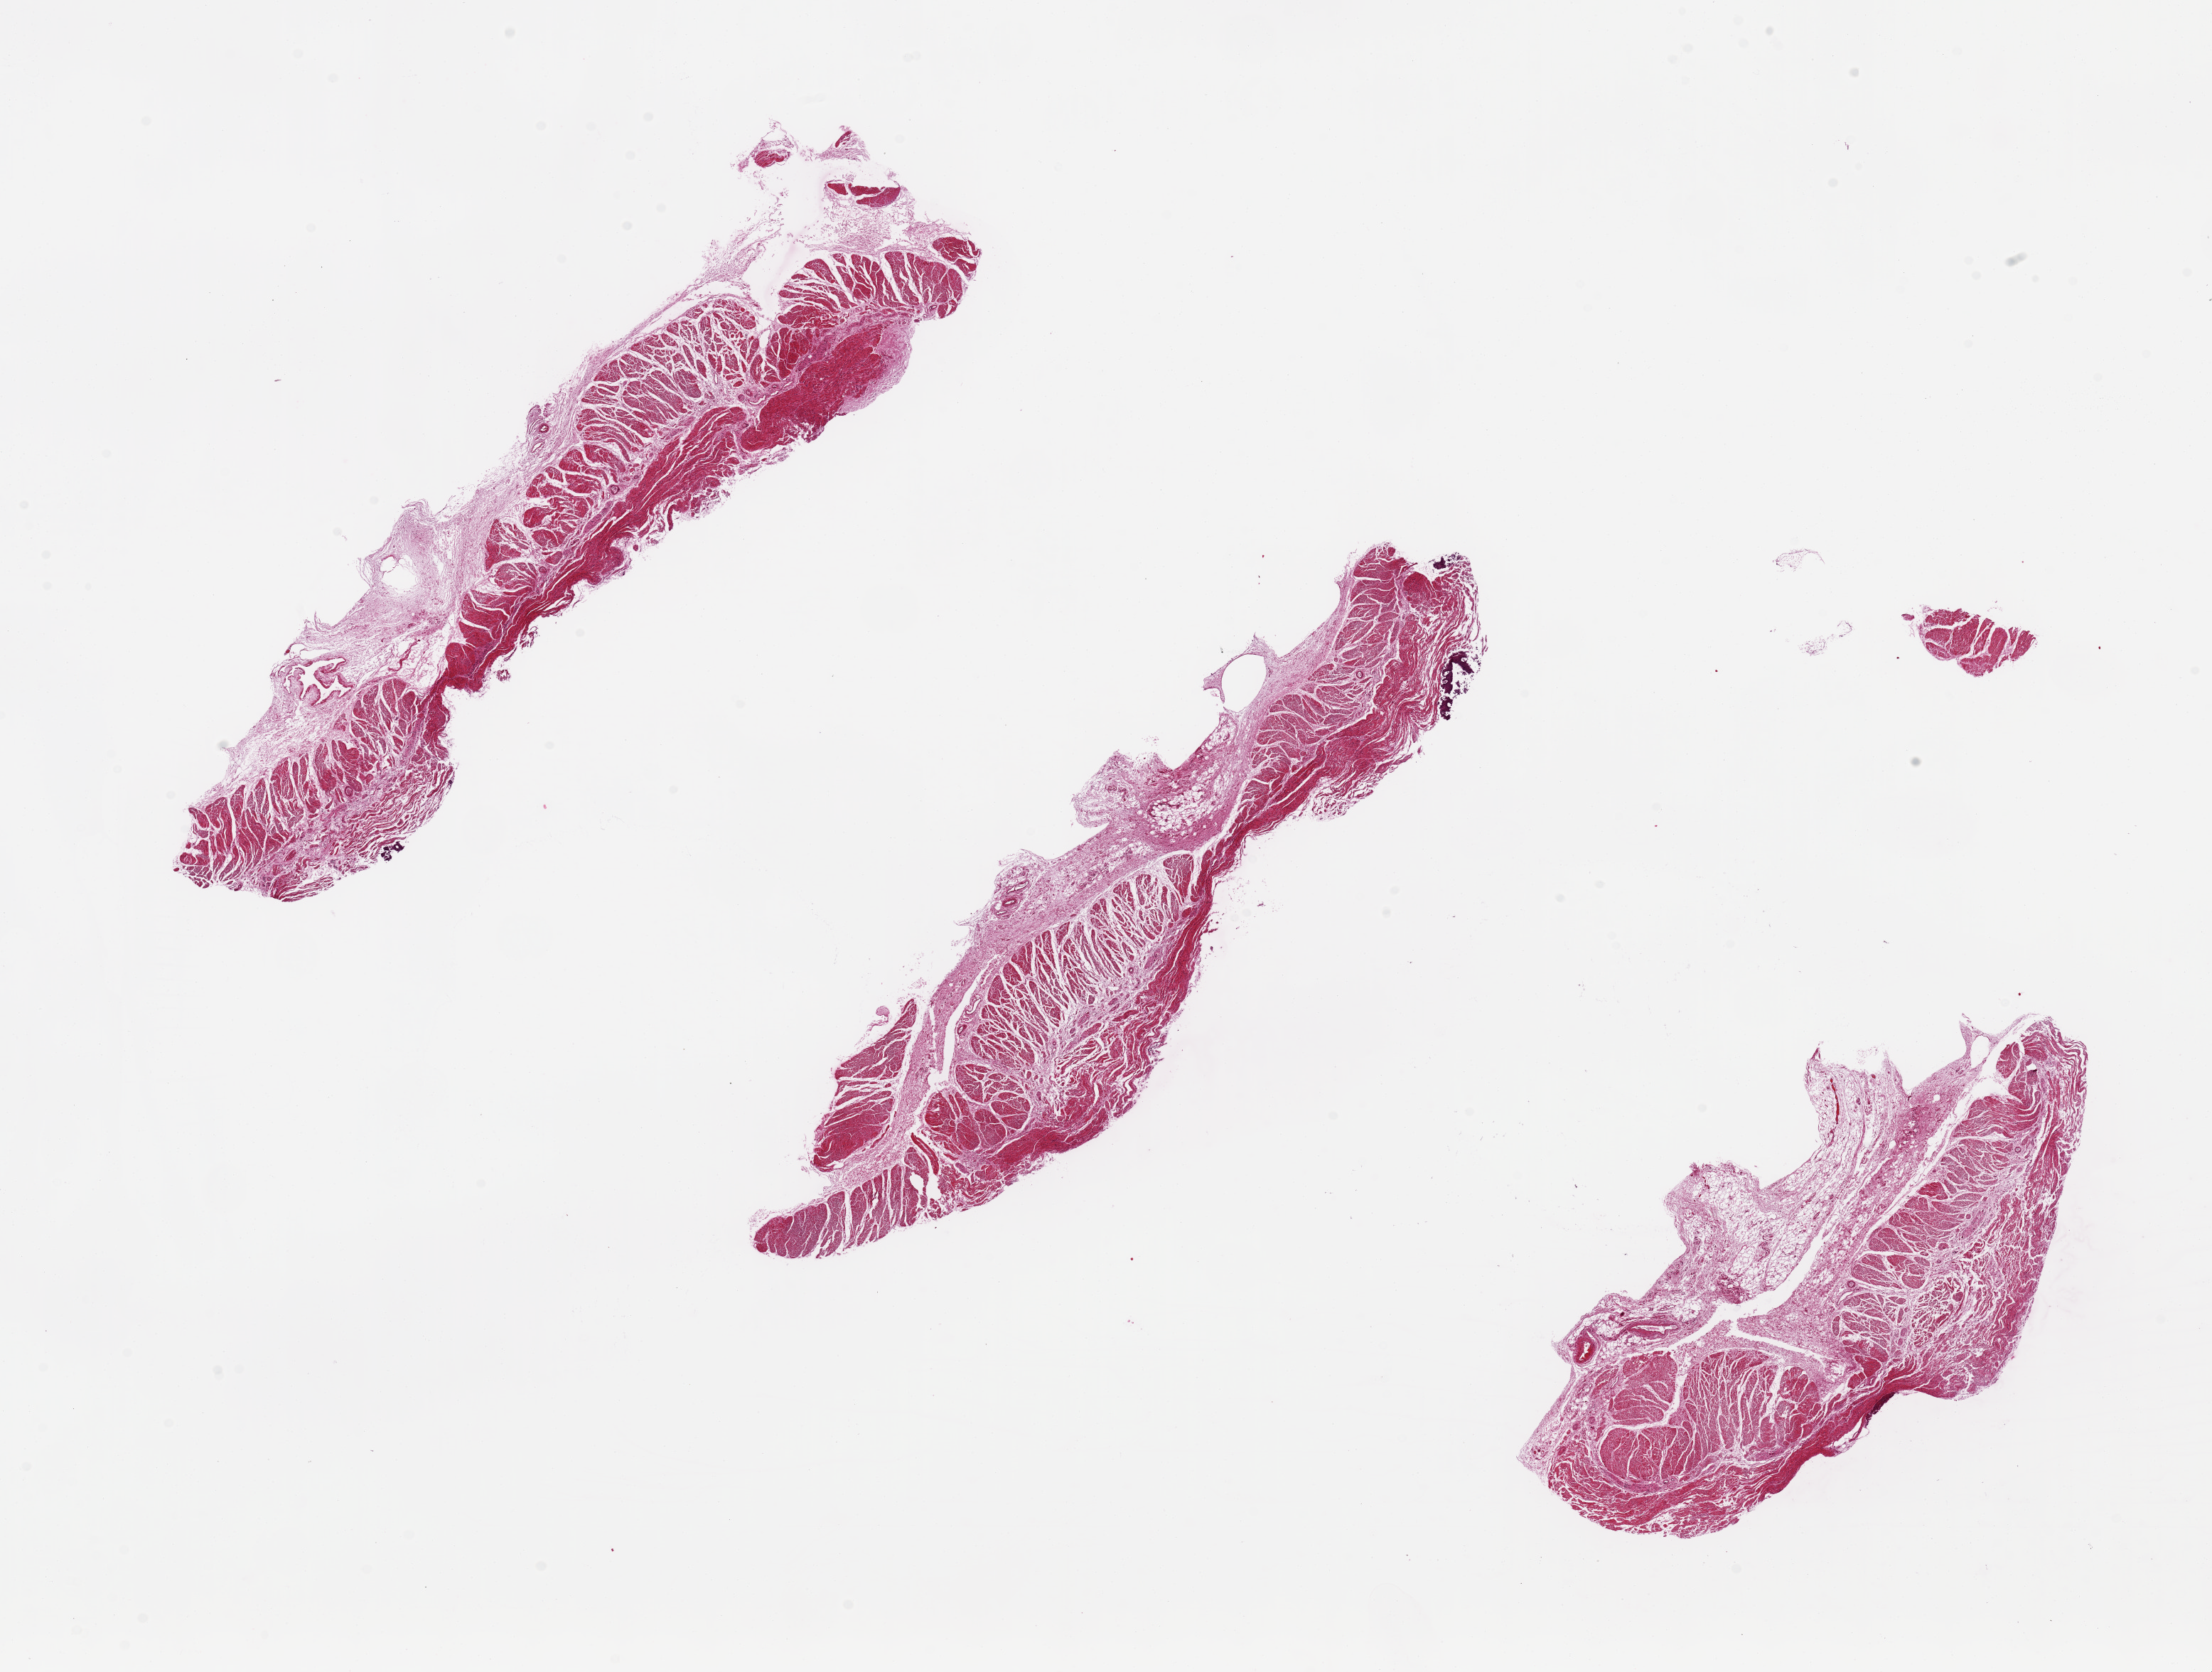
Whole-slide image, haematoxylin and eosin stain, brightfield, a low-resolution overview of the entire scanned area, about 24.6 x 18.6 mm (acquisition: 20x scan); PAXgene-fixed, paraffin-embedded tissue; target tissue: esophageal muscle; tissue donor sample. Donor sex: female.
Review note (as recorded): Minute focus of epithelium noted.